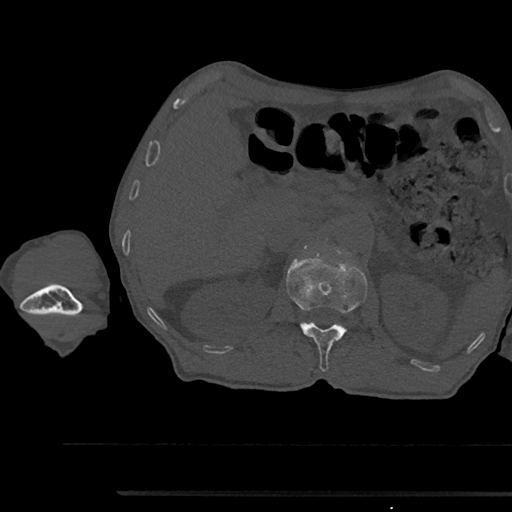
CT including the spine, one axial slice. Slice 629 of 797 in the series (ordered by position). Reconstruction kernel Br40s/3. 120 kVp. Bone window (W 1800 / L 400 HU). 512 × 512 image matrix. Patient: male, 79 years. Case-level facts recorded for this patient, not image findings: primary cancer: prostate.
Outlined on this slice (semi-automatically segmented with operator editing):
- L1 vertebra: box from (x=286, y=253) to (x=367, y=371) px